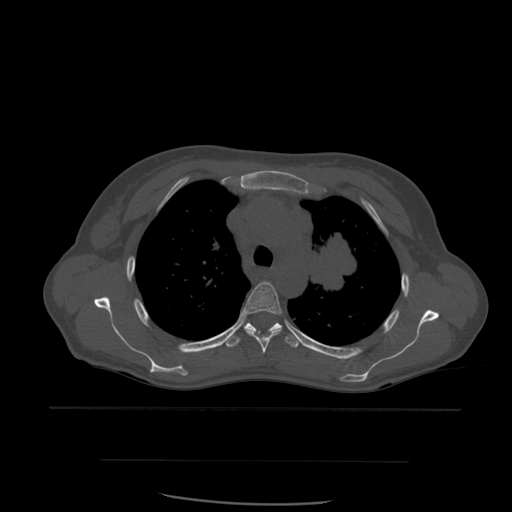
CT including the spine, one axial slice; slice 421 of 574 in the series (ordered by position); bone window (W 1800 / L 400 HU); 1.25 mm slice thickness; 512 × 512 image matrix, field of view 392 × 392 mm. Patient age 48 years. Case-level facts recorded for this patient, not image findings: primary cancer: lung.
Annotated regions visible in this slice (semi-automatically segmented with operator editing):
- T4 vertebra: box from (x=241, y=282) to (x=282, y=354) px
- T5 vertebra: (x=225, y=323)–(x=302, y=348)